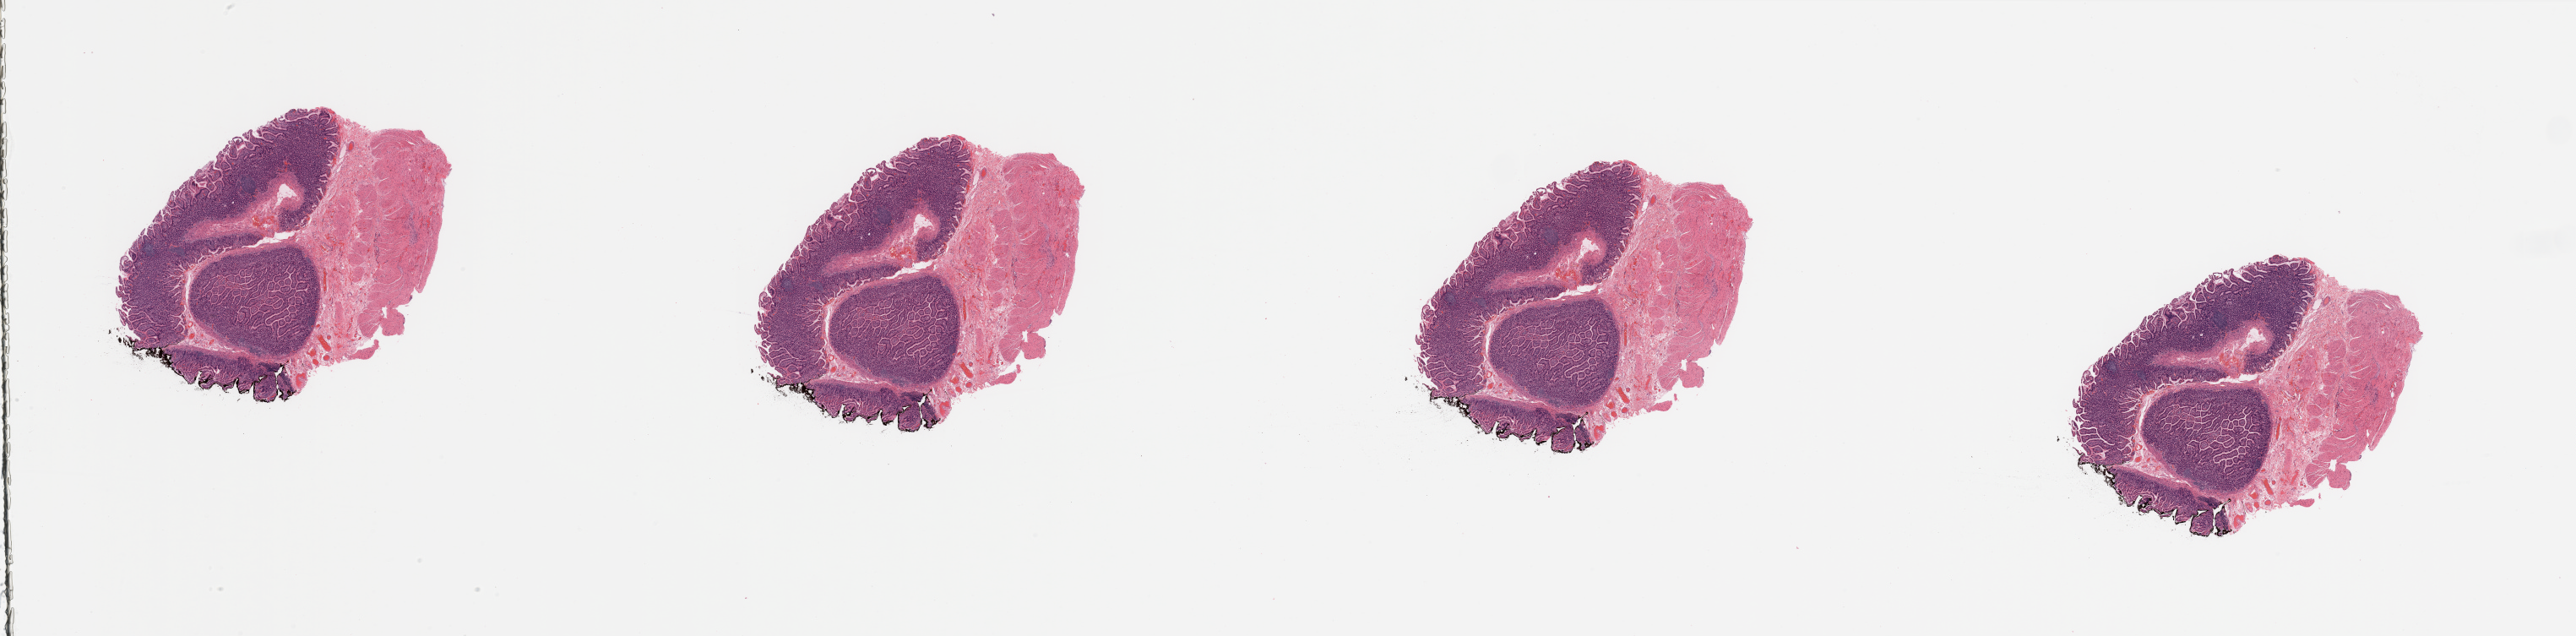
Whole-slide histology image, H&E, whole scanned area (about 48.2 x 11.9 mm) shown as a low-resolution overview; normal (non-tumour) tissue sample, sampled site: pancreas. 62-year-old male patient.
This section: normal (non-tumour) tissue from the same patient. Patient diagnosis: Infiltrating duct carcinoma, NOS.